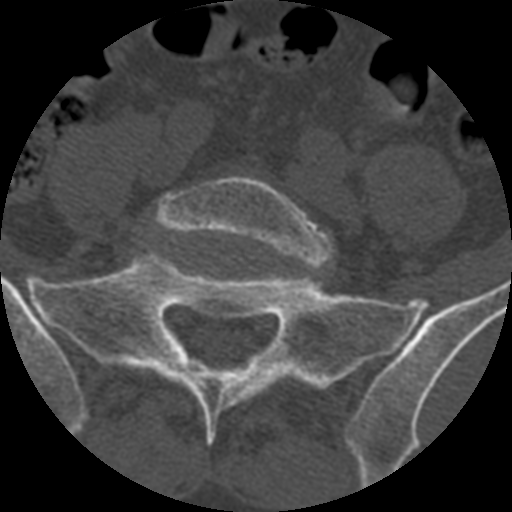
CT including the spine, one axial slice; slice 241 of 399 in the series (ordered by position); reconstruction kernel STANDARD; bone window (W 1800 / L 400 HU); 1.25 mm slice thickness; 512 × 512 image matrix, field of view 160 × 160 mm. Patient age 71 years. Case-level facts recorded for this patient, not image findings: primary cancer: prostate.
Outlined on this slice (semi-automatically segmented with operator editing):
- L5 vertebra: bounding box <152,176,335,267> (left, top, right, bottom; pixels)